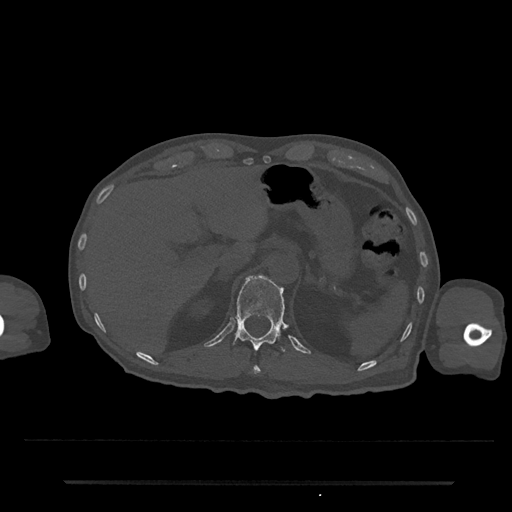
CT including the spine, one axial slice. 120 kVp. Bone window (W 1800 / L 400 HU). 512 × 512 image matrix, field of view 427 × 427 mm. Patient: male, 74 years. Case-level facts recorded for this patient, not image findings: primary cancer: prostate.
Structures marked on this image (semi-automatic segmentation, software-assisted and operator-edited):
- T11 vertebra: box from (x=252, y=365) to (x=261, y=375) px
- T12 vertebra: (x=233, y=277)–(x=286, y=351)